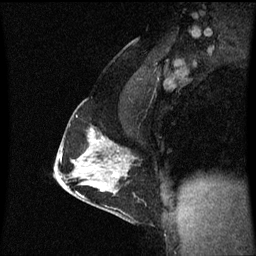
Breast MRI (dynamic contrast-enhanced), one sagittal slice; position 37 of 60 along the scan axis; dynamic contrast-enhanced series, image 2 of 3 at this slice position (ordered by acquisition); 1.5 T; TE 4.2 ms, TR 8.9 ms; 2 mm slice thickness; 256 × 256 image matrix. Female patient, age 47 years. Case-level facts recorded for this patient, not image findings: setting: breast cancer imaged before/during neoadjuvant chemotherapy; receptor status: HR-positive, HER2-negative.
Annotated regions visible in this slice (semi-automatically segmented with operator editing):
- analysis volume of interest (the breast-tissue region the enhancement analysis was run in; not a lesion): bounding box [x1, y1, x2, y2] px = [56, 110, 138, 209]
- tumour enhancement mask (voxels above the 70 % enhancement threshold inside the analysis volume of interest): [90, 130, 119, 177]